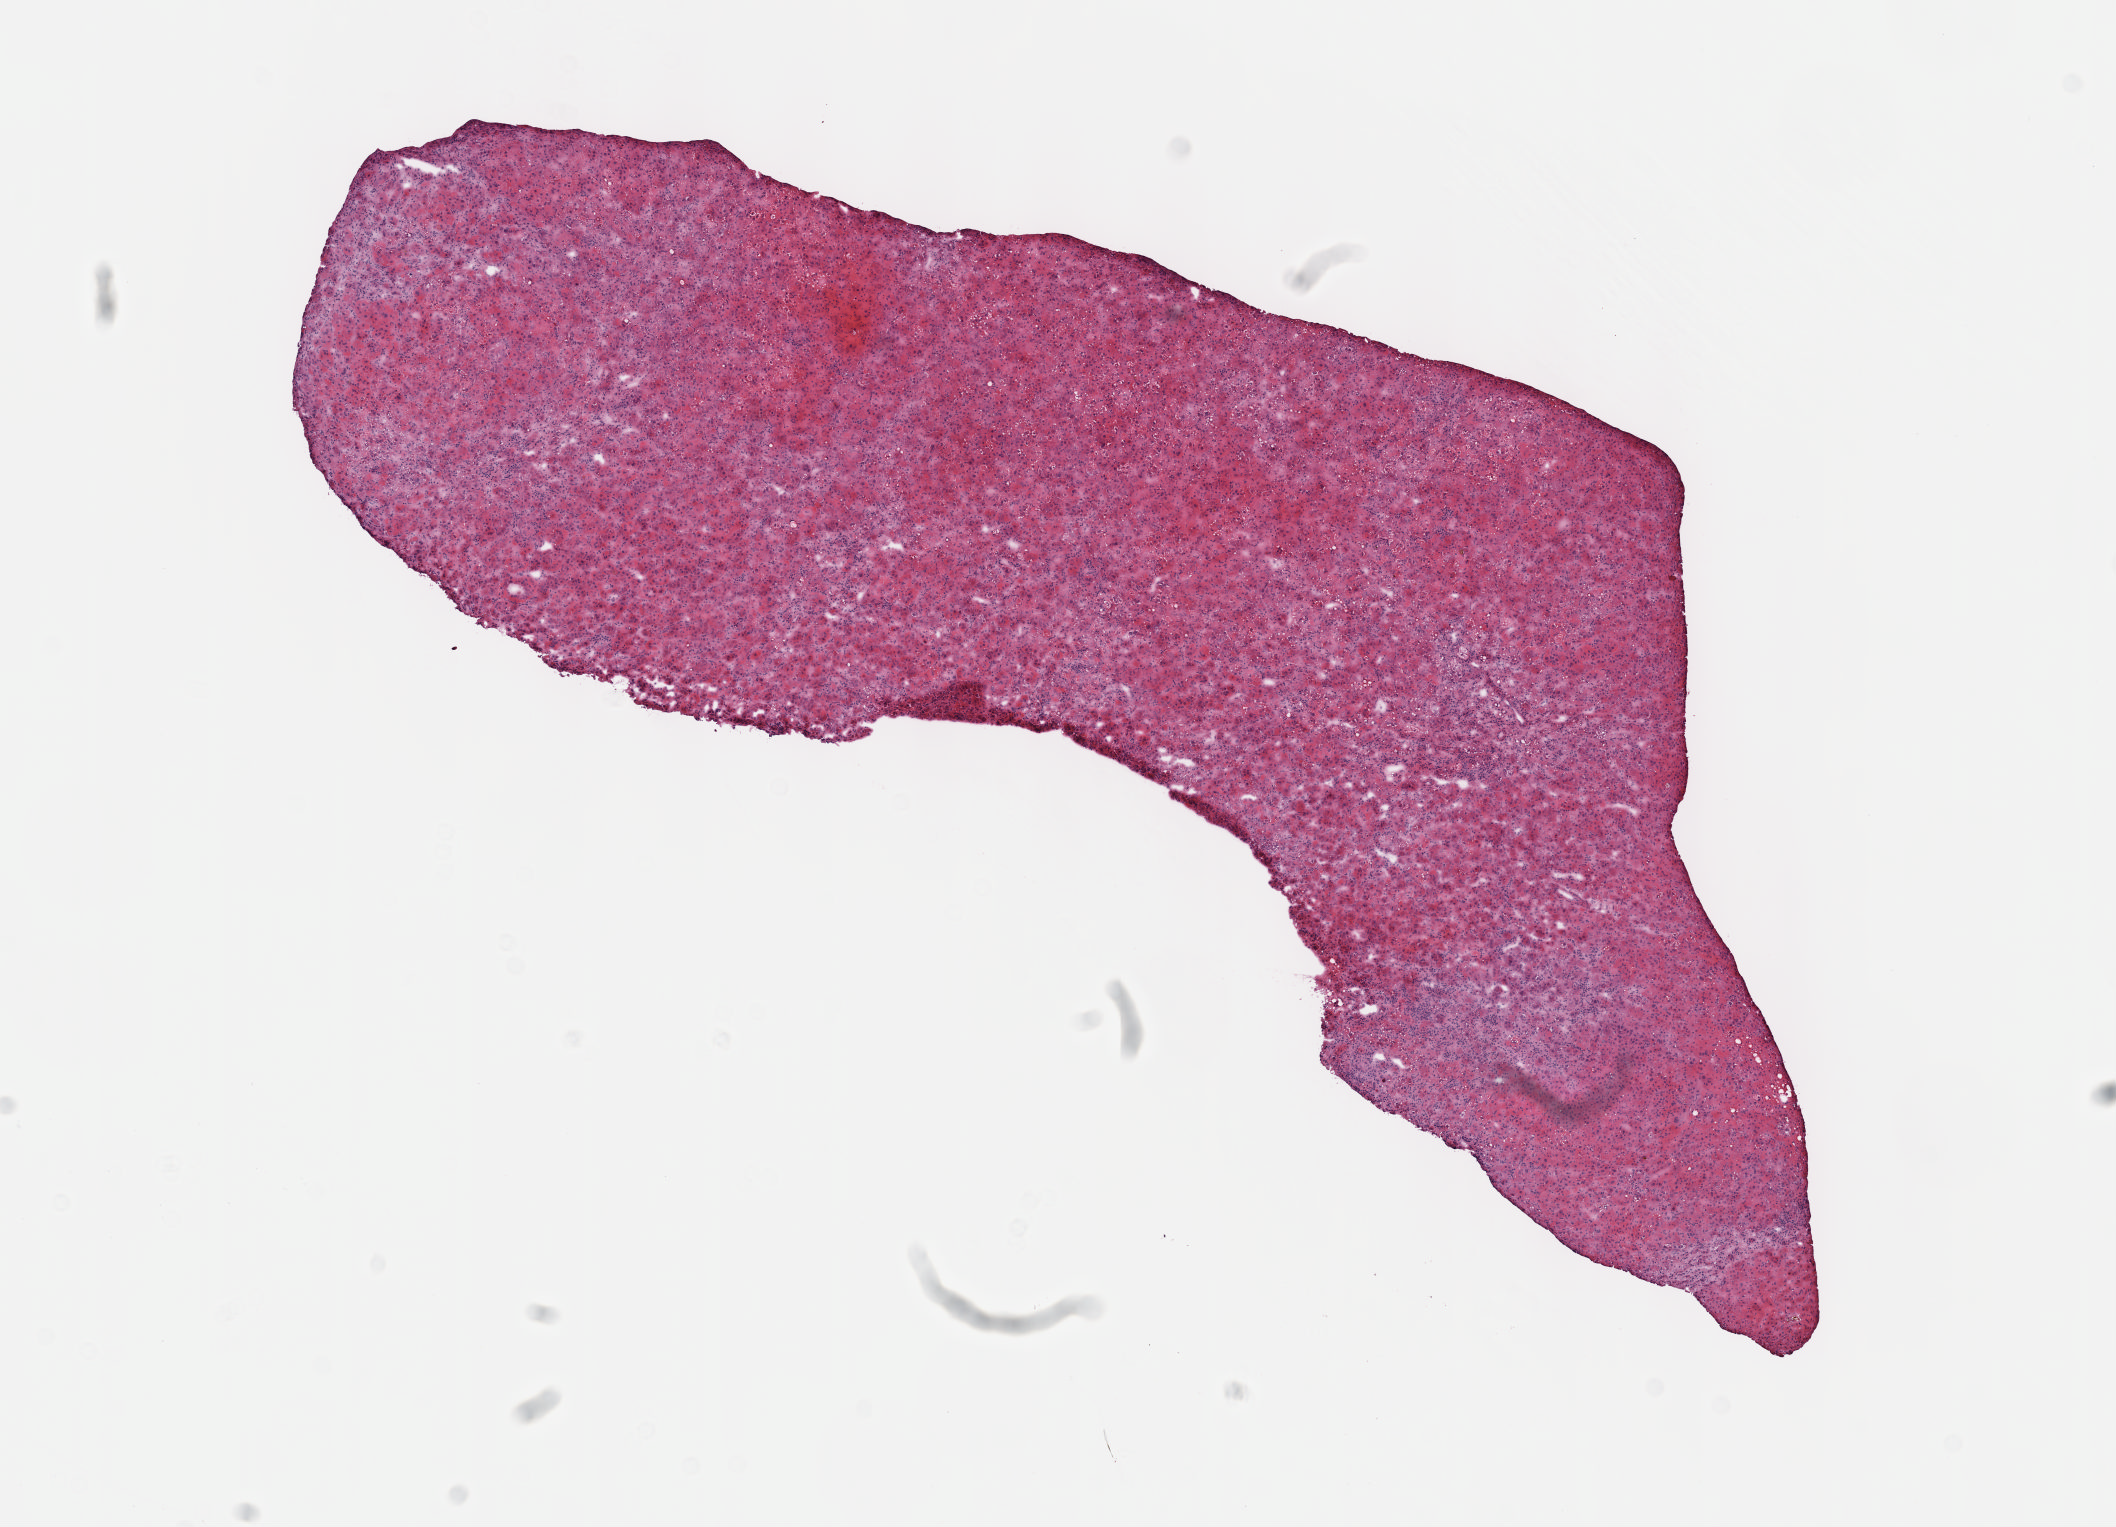
Hematoxylin and eosin (H&E) stained whole-slide image, a low-resolution overview of the entire scanned area, about 8.6 x 6.2 mm (acquisition: 40x scan). Frozen section. Sample: primary tumour, liver. Male, age 45 years at initial diagnosis. Histologic grade: G3 (poorly differentiated). Slide review estimates, as recorded: tumour cells 100%, tumour nuclei 80%, normal cells 0%, stromal cells 0%, necrosis 0%. Infiltration values recorded for this section: lymphocyte infiltration 2%, monocyte infiltration 0%, neutrophil infiltration 0%.
Pathologic diagnosis: Hepatocellular carcinoma, NOS. AJCC pathologic stage: I (7th edition). TNM: T1 N0 M0.